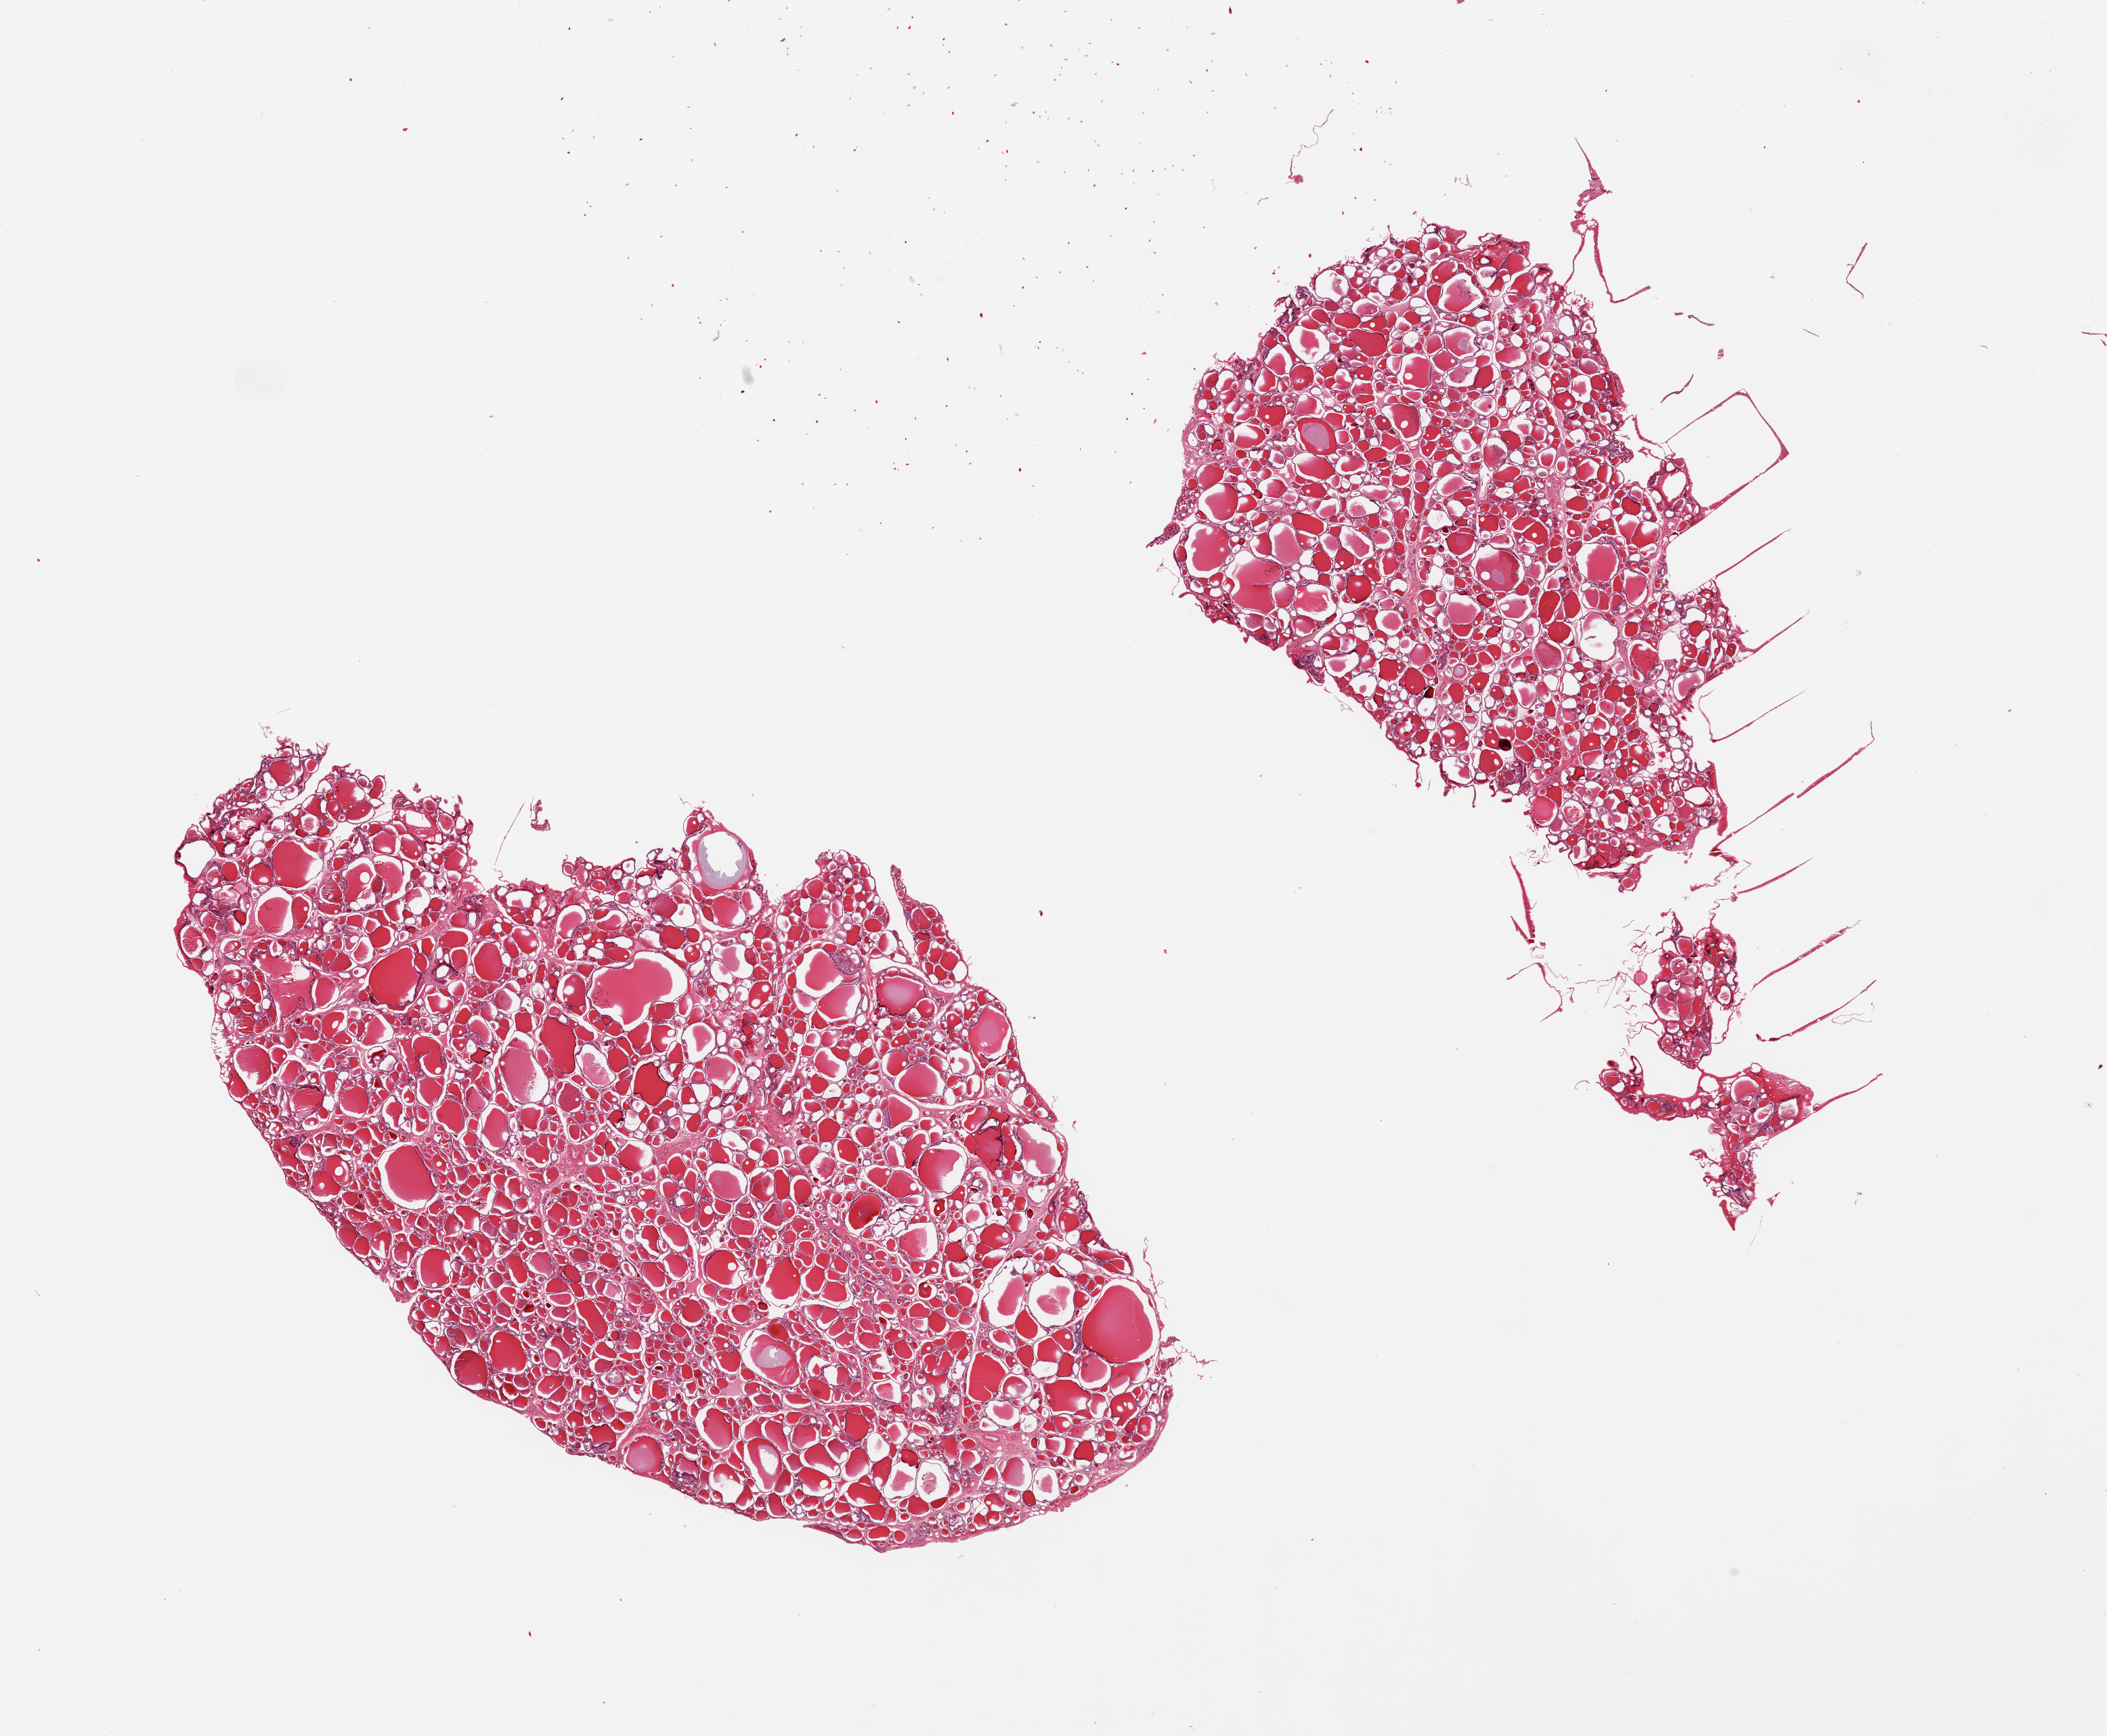
Digitized hematoxylin and eosin (H&E)-stained section — whole scanned area (about 24.6 x 20.3 mm, slide scanned at 20x) shown as a low-resolution overview, PAXgene-fixed, paraffin-embedded tissue, sampled site (target tissue): thyroid, tissue donor sample. Donor: female.
Review note (as recorded): 2 pieces.